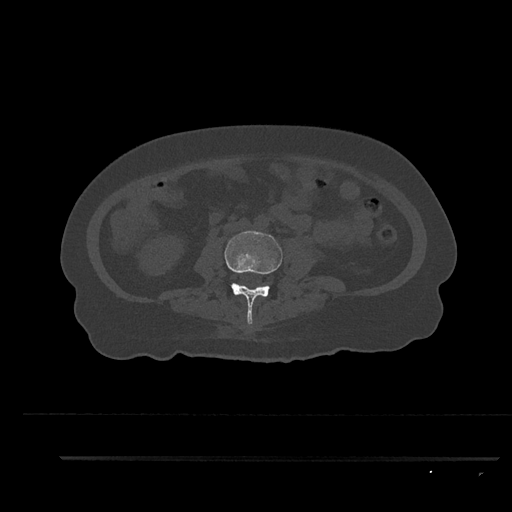
CT including the spine, one axial slice; slice 76 of 797 in the series (ordered by position); bone window (W 1800 / L 400 HU); 0.5 mm slice thickness; 512 × 512 image matrix, field of view 408 × 408 mm. Patient: female, 44 years. Case-level facts recorded for this patient, not image findings: primary cancer: renal.
Outlined on this slice (semi-automatic segmentation, software-assisted and operator-edited):
- L3 vertebra: bounding box <224,231,283,325> (left, top, right, bottom; pixels)